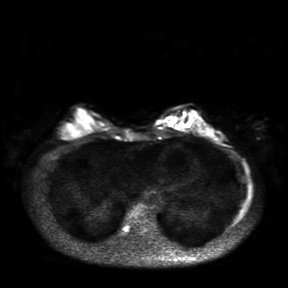
Breast MRI, one axial slice; slice 10 of 30 in the series (ordered by position); diffusion-weighted series; image 2 of 4 stored at this slice position (different b-values; order by instance number); 3 T; 4 mm slice thickness; 288 × 288 image matrix, field of view 360 × 360 mm. Female patient.
Structures marked on this image (outlined manually by an expert reader):
- tumour on diffusion-weighted imaging: bounding box [x1, y1, x2, y2] px = [164, 119, 168, 123]